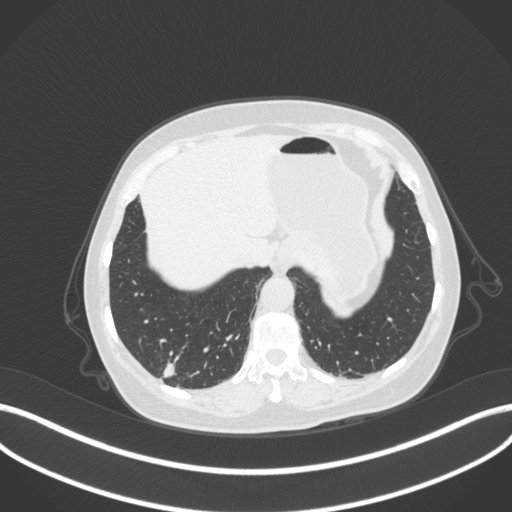
Chest CT, one axial slice; position 47 of 340 along the scan axis; reconstruction kernel B31f; 120 kVp; lung window (W 1500 / L -600 HU); 1 mm slice thickness; 512 × 512 image matrix, field of view 400 × 400 mm. Female patient, age 69 years. From the clinical record (not read from this slice): clinical TNM (as recorded): T1b N0 M0; histopathological grade: G2-3.
Annotated regions visible in this slice (bounding box drawn by a radiologist):
- lung tumour (recorded histology: adenocarcinoma): bounding box (x1, y1, x2, y2) in pixels: (161, 357, 178, 382)